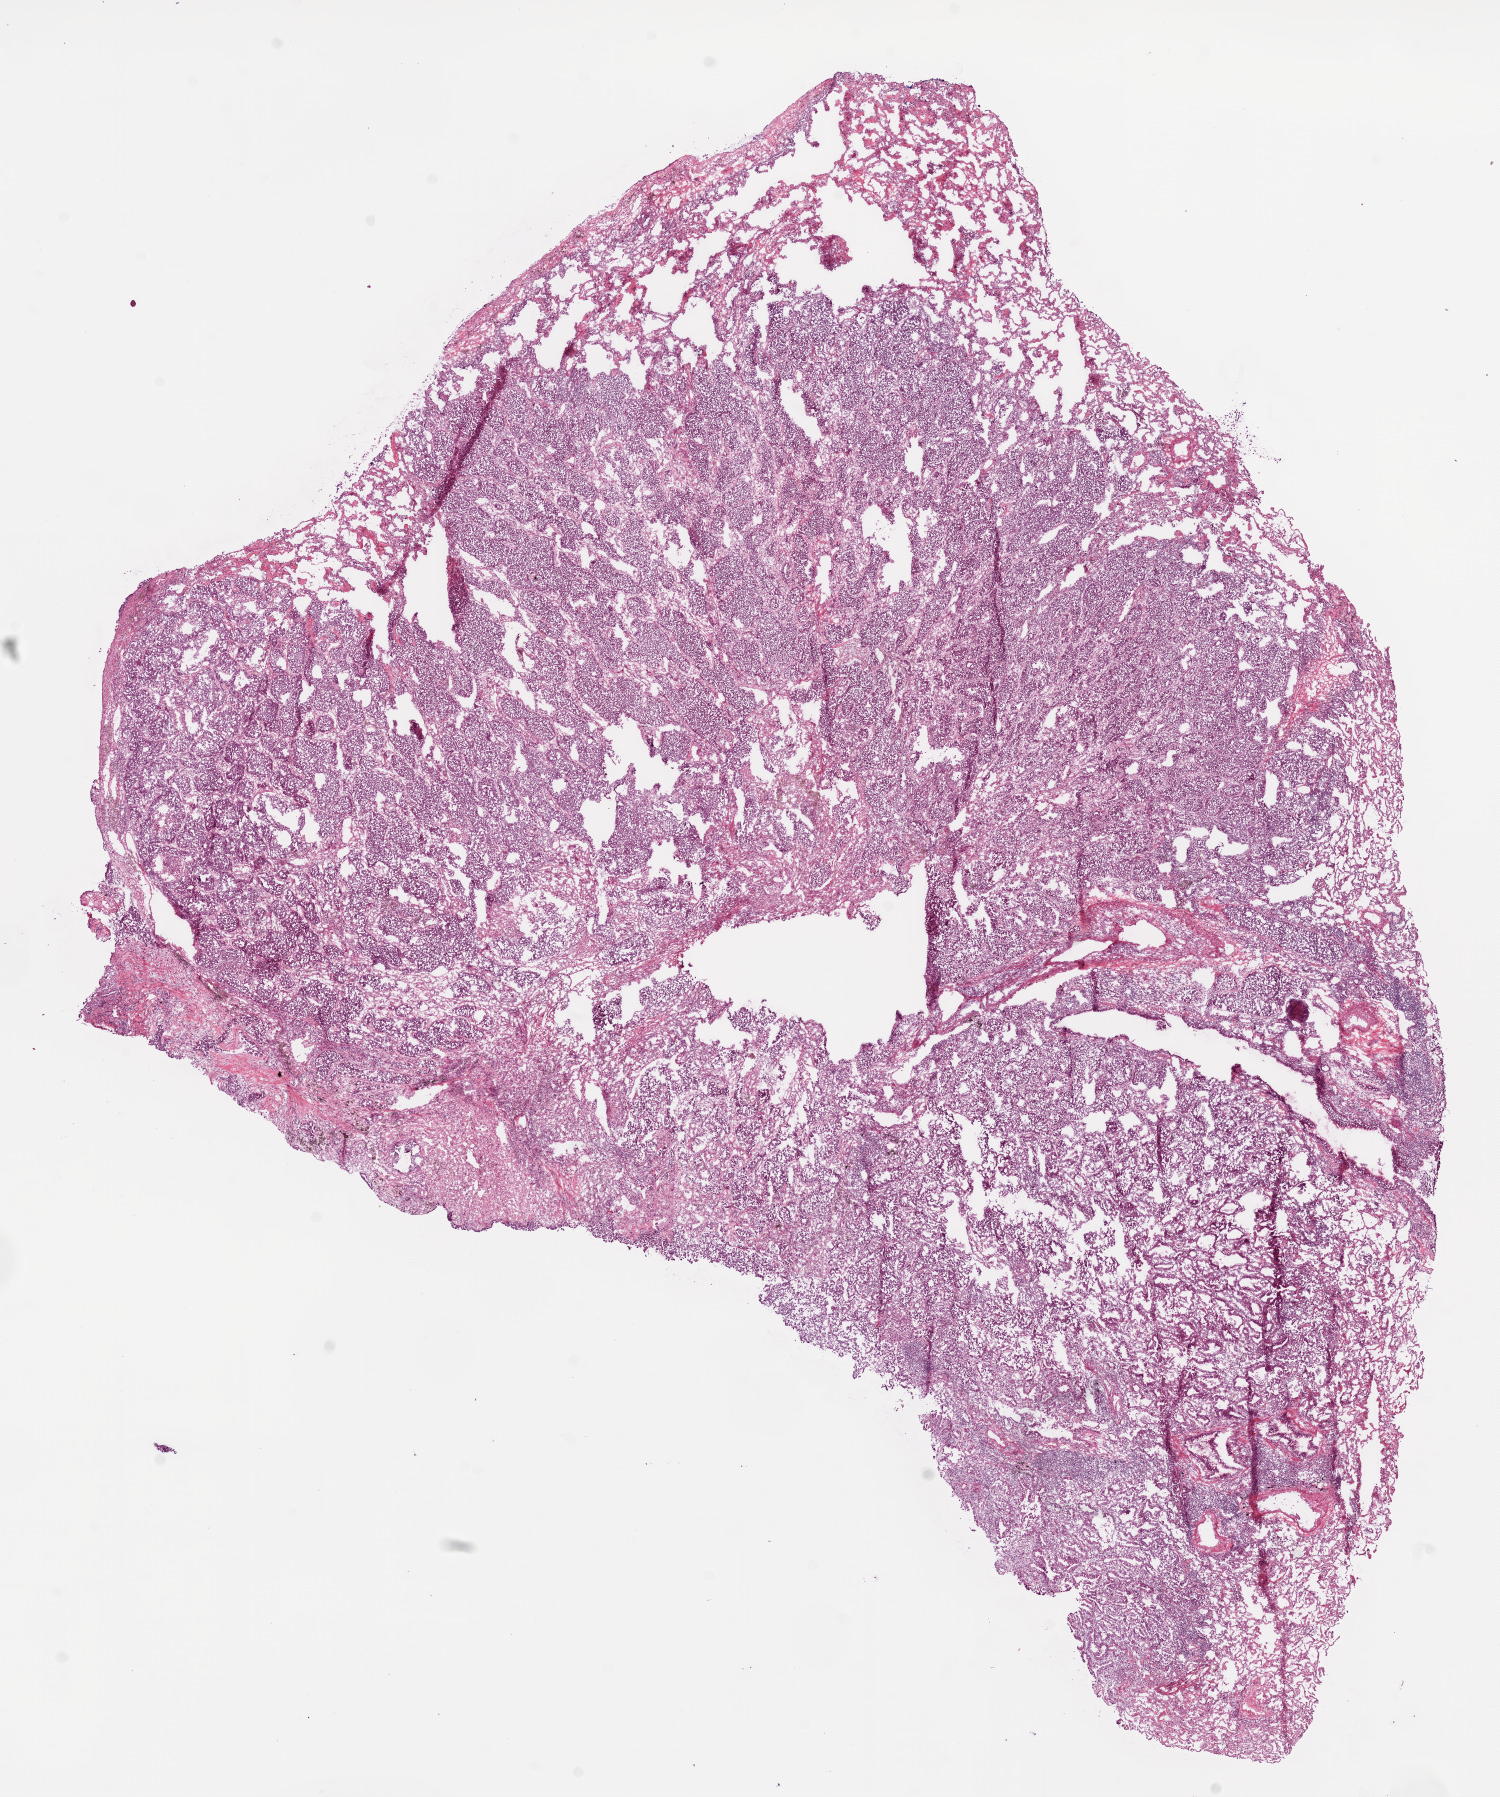
Digitized Hematoxylin and eosin (H&E) stained tissue section (whole slide) — low-resolution overview of the scanned area, about 12.0 x 14.4 mm, frozen section, sample: primary tumour, lung. Female patient; age at initial diagnosis 42 years. Pathologist review of this section (percent, as recorded): tumour cells 80%, tumour nuclei 80%, normal cells 10%, stromal cells 10%, necrosis 0%.
Histologic diagnosis: Adenocarcinoma, NOS. AJCC pathologic stage: IIIA (6th edition). TNM: T2 N2 M0. Laterality: left.